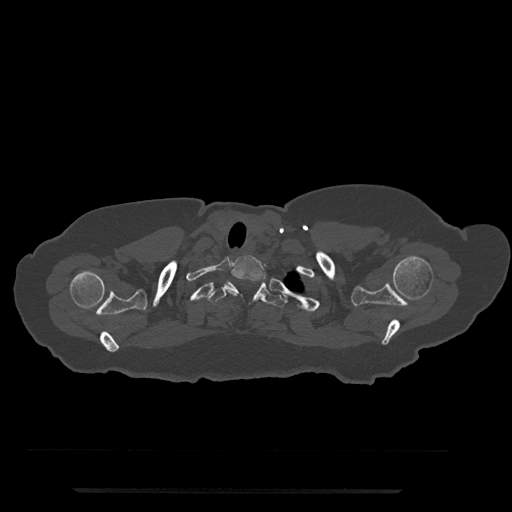
CT including the spine, one axial slice; position 690 of 797 along the scan axis; bone window (W 1800 / L 400 HU); 512 × 512 image matrix, field of view 440 × 440 mm. Female patient, age 51 years. Case-level facts recorded for this patient, not image findings: primary cancer: neuro; vertebrae with lytic lesions (as recorded): T8.
Annotated regions visible in this slice (semi-automatic segmentation, software-assisted and operator-edited):
- T1 vertebra: bounding box [x1, y1, x2, y2] px = [231, 255, 266, 296]
- T2 vertebra: [206, 281, 286, 308]